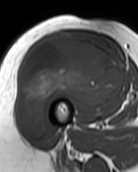
MRI of an extremity soft-tissue mass, one axial slice; slice 51 of 99 in the series (ordered by position); MR volume resampled by the dataset authors to the PET/CT grid (not the native acquisition matrix); 3.27 mm slice thickness; 138 × 172 image matrix, field of view 135 × 168 mm. Female patient. Case-level facts recorded for this patient, not image findings: histological type: pleiomorphic undifferentiated sarcoma; grade: high; site of the primary tumour: right quadricep.
Annotated regions visible in this slice (expert contour drawn on MRI and transferred to this co-registered scan by the dataset authors):
- gross tumour volume including surrounding oedema: bounding box (x1, y1, x2, y2) in pixels: (18, 32, 125, 138)
- gross tumour volume (mass): (18, 32, 125, 138)